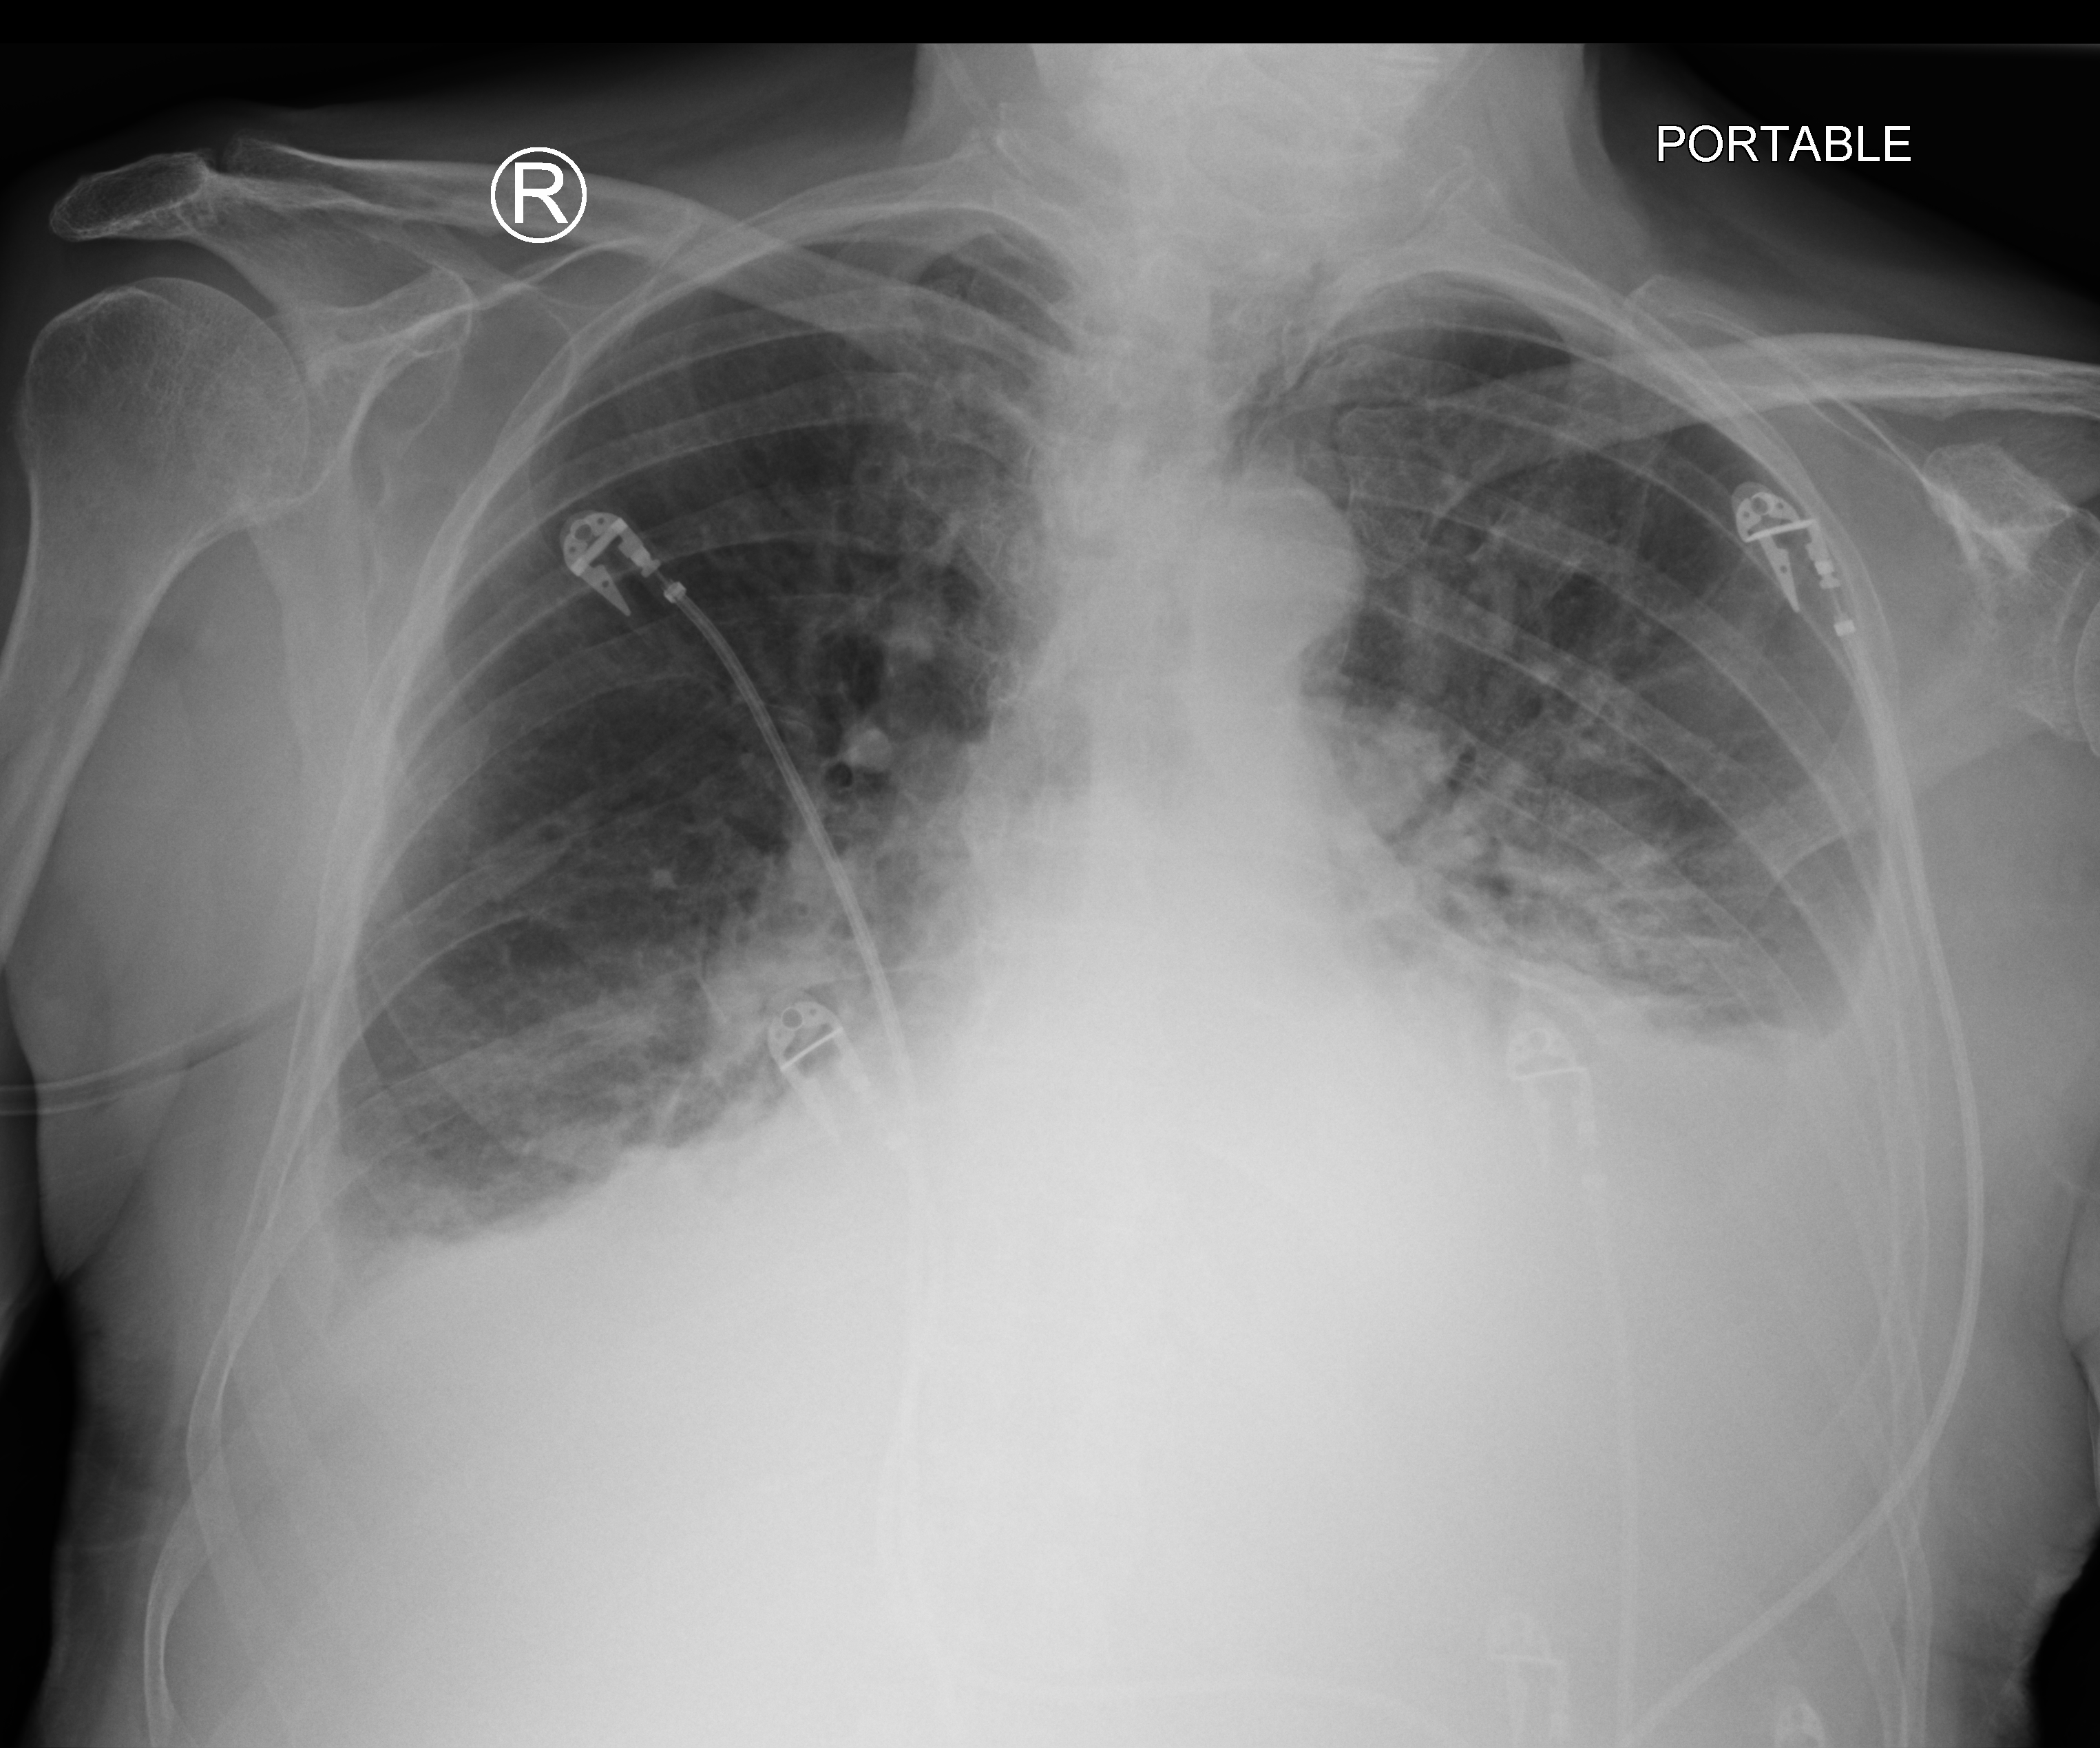
Bedside chest radiograph (computed radiography); anteroposterior (AP) projection. Patient hospitalised with COVID-19; male, aged 75–90 years.
Hospital-stay facts (about this admission, not read from this image; timing relative to this image not recorded): mechanically ventilated during this hospital stay: no; admitted to intensive care during this hospital stay: no.